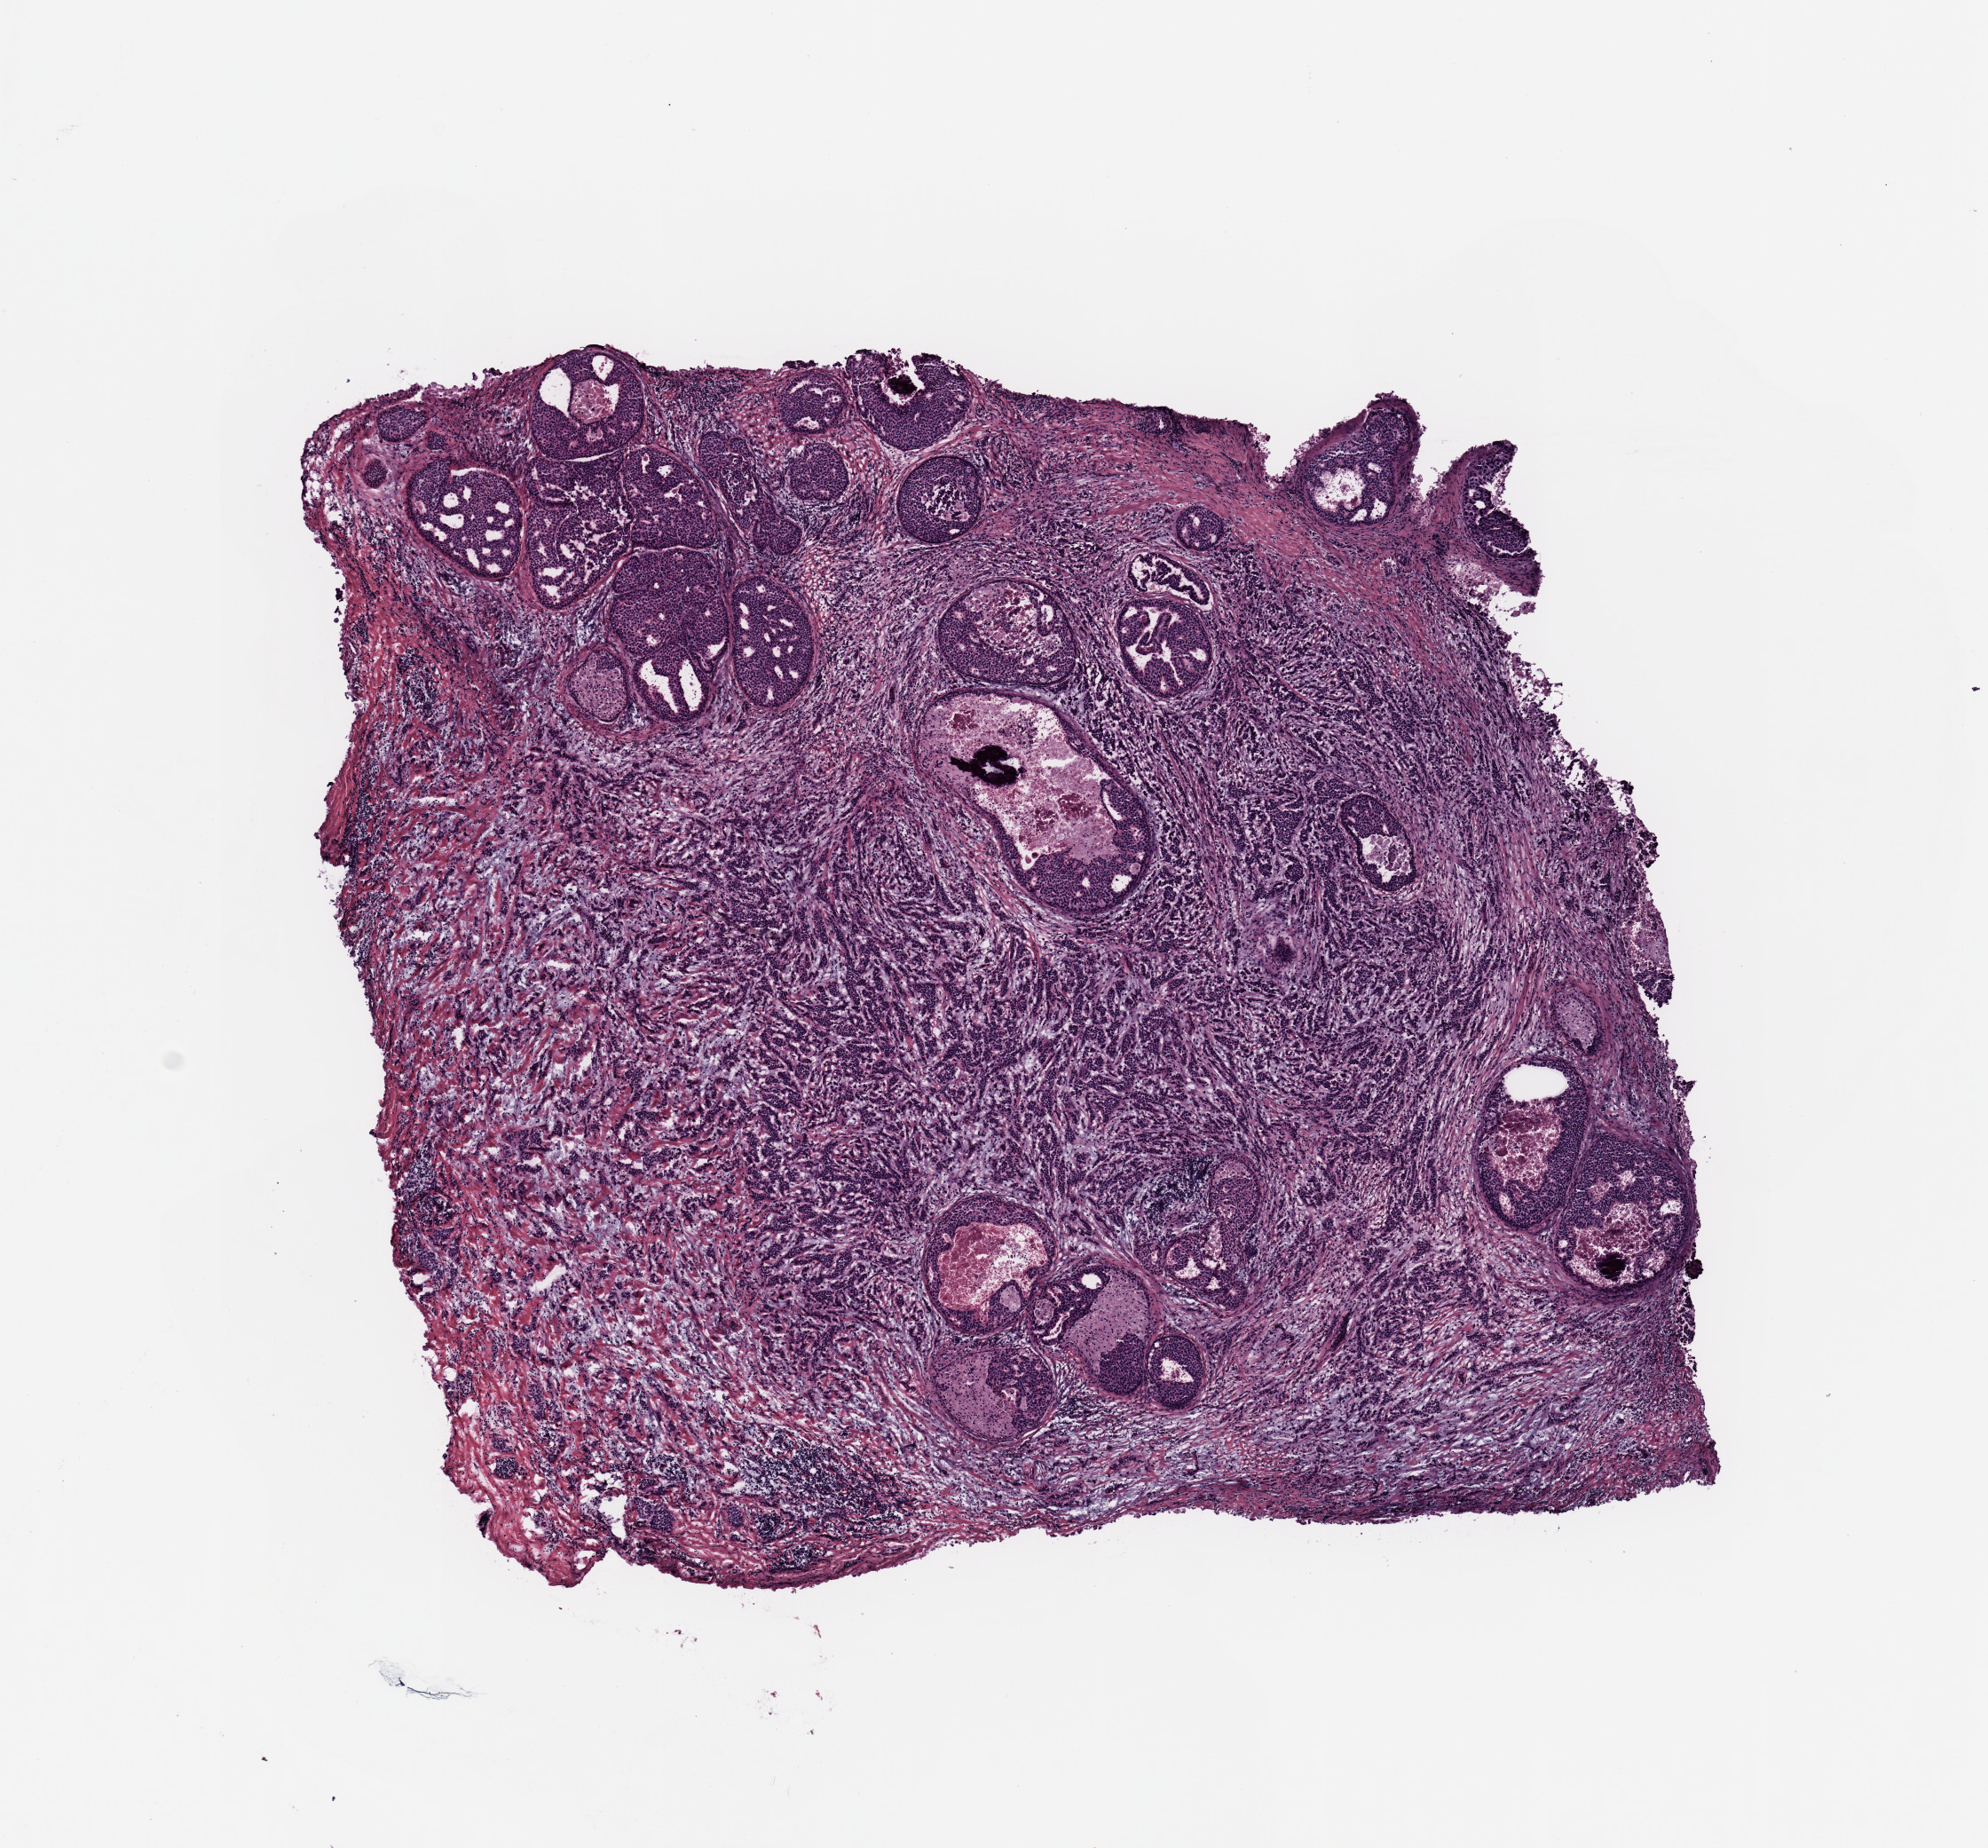
Whole-slide histology image, H&E-stained — whole scanned area (about 8.9 x 8.2 mm, acquisition: 20x scan) shown as a low-resolution overview; breast, tissue type not recorded.
Patient diagnosis (cohort enrolment): breast cancer (breast).